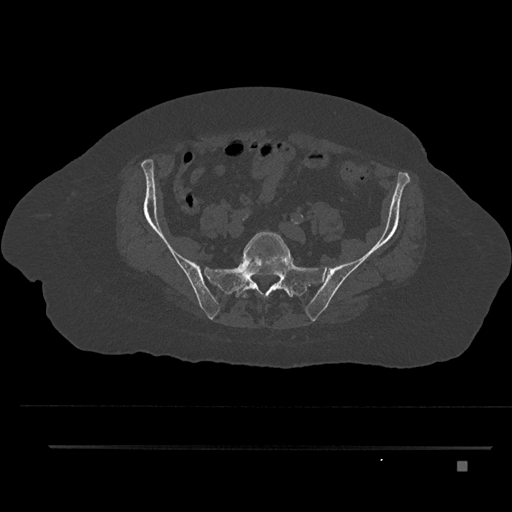
CT including the spine, one axial slice. Slice 14 of 797 in the series (ordered by position). Reconstruction kernel Br40s/3. 120 kVp. Bone window (W 1800 / L 400 HU). 0.5 mm slice thickness. 512 × 512 image matrix. Female patient, age 76 years. From the clinical record (not read from this slice): primary cancer: lung; vertebrae with lytic lesions (as recorded): T11, L3.
Outlined on this slice (semi-automatically segmented with operator editing):
- L5 vertebra: bounding box <242,231,290,298> (left, top, right, bottom; pixels)